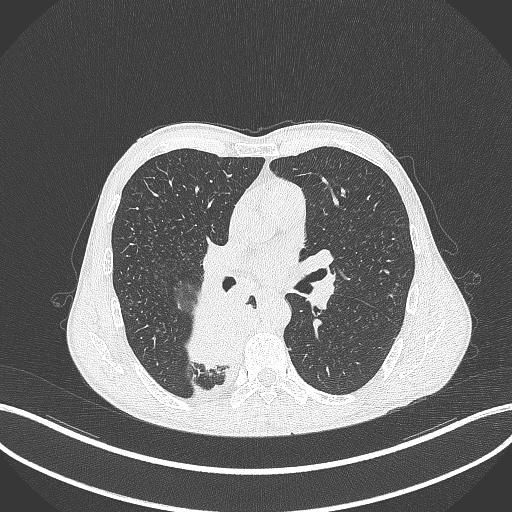
Chest CT, one axial slice; position 208 of 371 along the scan axis; reconstruction kernel B70f; 120 kVp; lung window (W 1500 / L -600 HU); 1 mm slice thickness; 512 × 512 image matrix. Male patient, age 58 years. From the clinical record (not read from this slice): clinical TNM (as recorded): T3 N1 M1.
Outlined on this slice (bounding box drawn by a radiologist):
- lung tumour (recorded histology: squamous cell carcinoma): box from (x=187, y=282) to (x=248, y=370) px